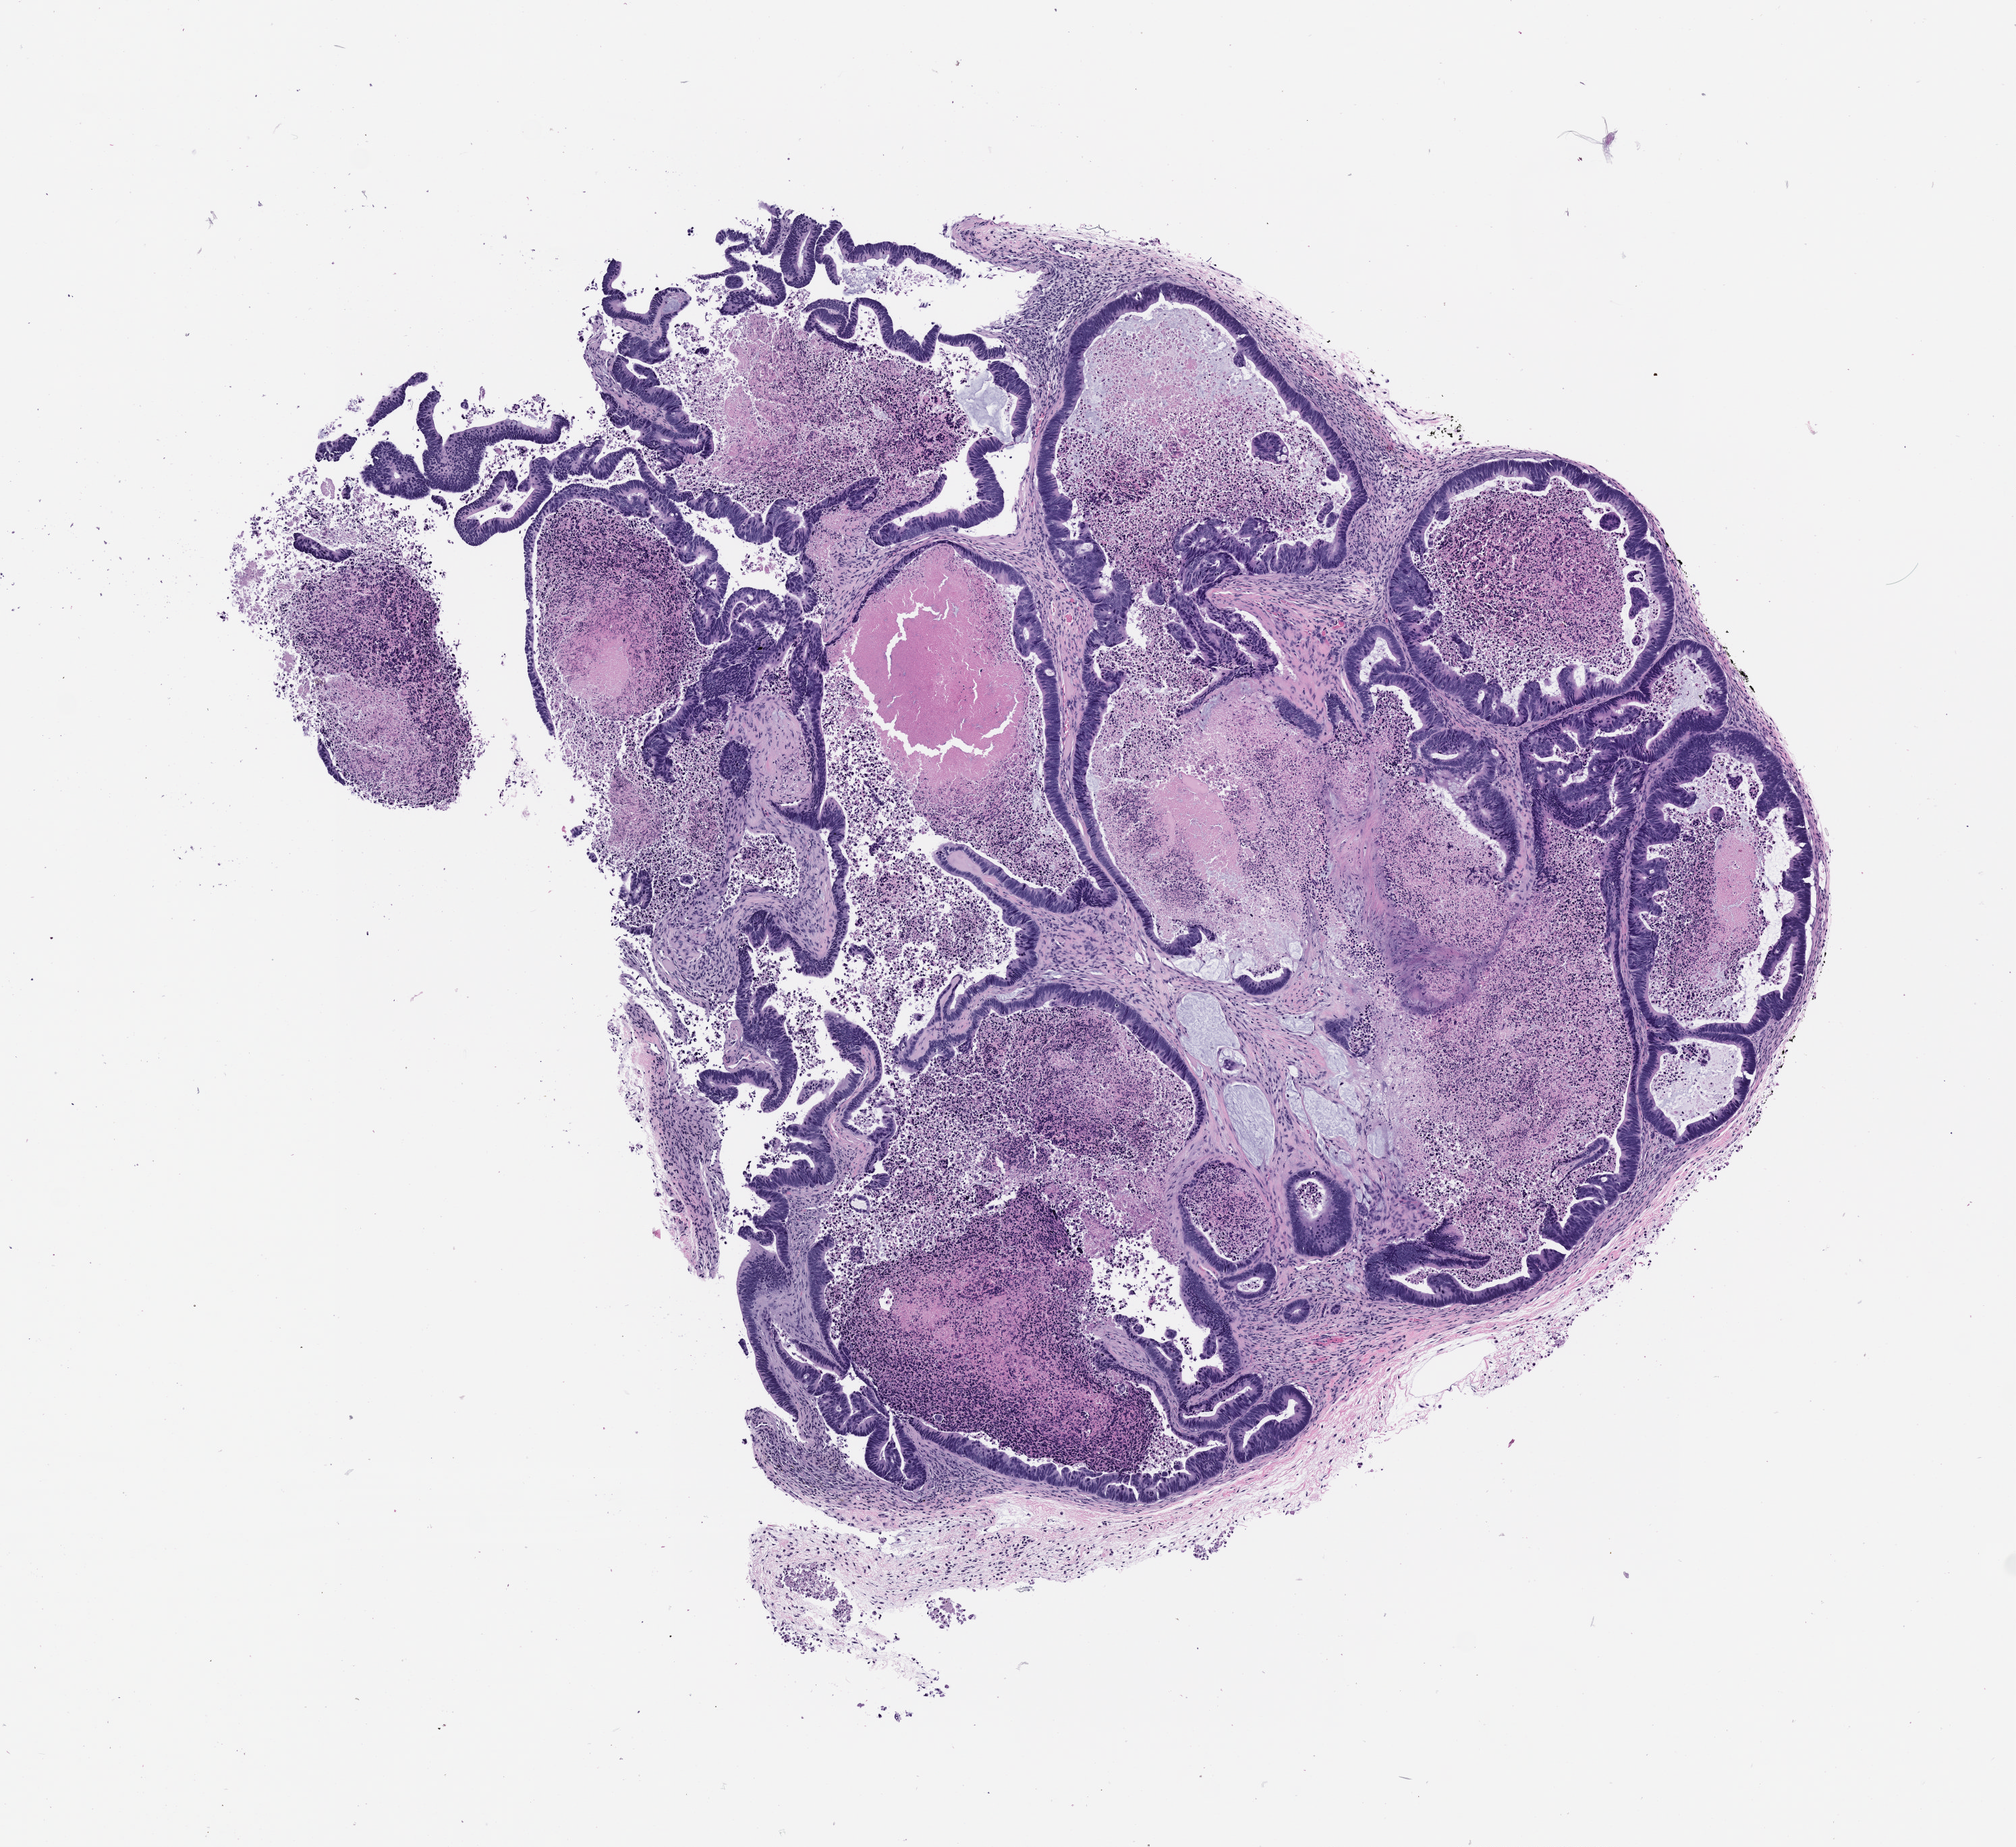
Whole-slide image, H&E: patient-derived xenograft (human tumor grown in a mouse), passage 0 — whole scanned area (about 6.0 x 5.5 mm) shown as a low-resolution overview, formalin-fixed, paraffin-embedded (FFPE) tissue, originating tumor site category: colon.
Originating patient diagnosis: Colon Adenocarcinoma.